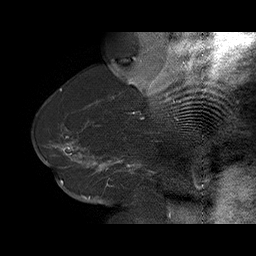
Breast MRI (dynamic contrast-enhanced), one sagittal slice. Slice 46 of 75 in the series (ordered by position). Dynamic contrast-enhanced series, time point 2 of 6 at this slice position (early post-contrast). 1.5 T. TE 4.5 ms, TR 32.4 ms. 3 mm slice thickness. 256 × 256 image matrix, field of view 180 × 180 mm. Female patient. Case-level facts recorded for this patient, not image findings: setting: breast cancer imaged before/during neoadjuvant chemotherapy; receptor status: HR-positive, HER2-negative.
Annotated regions visible in this slice (semi-automatic segmentation, software-assisted and operator-edited):
- analysis volume of interest (the breast-tissue region the enhancement analysis was run in; not a lesion): box from (x=58, y=134) to (x=166, y=191) px
- tumour enhancement mask (voxels above the 100 % enhancement threshold inside the analysis volume of interest): (x=59, y=142)–(x=150, y=182)